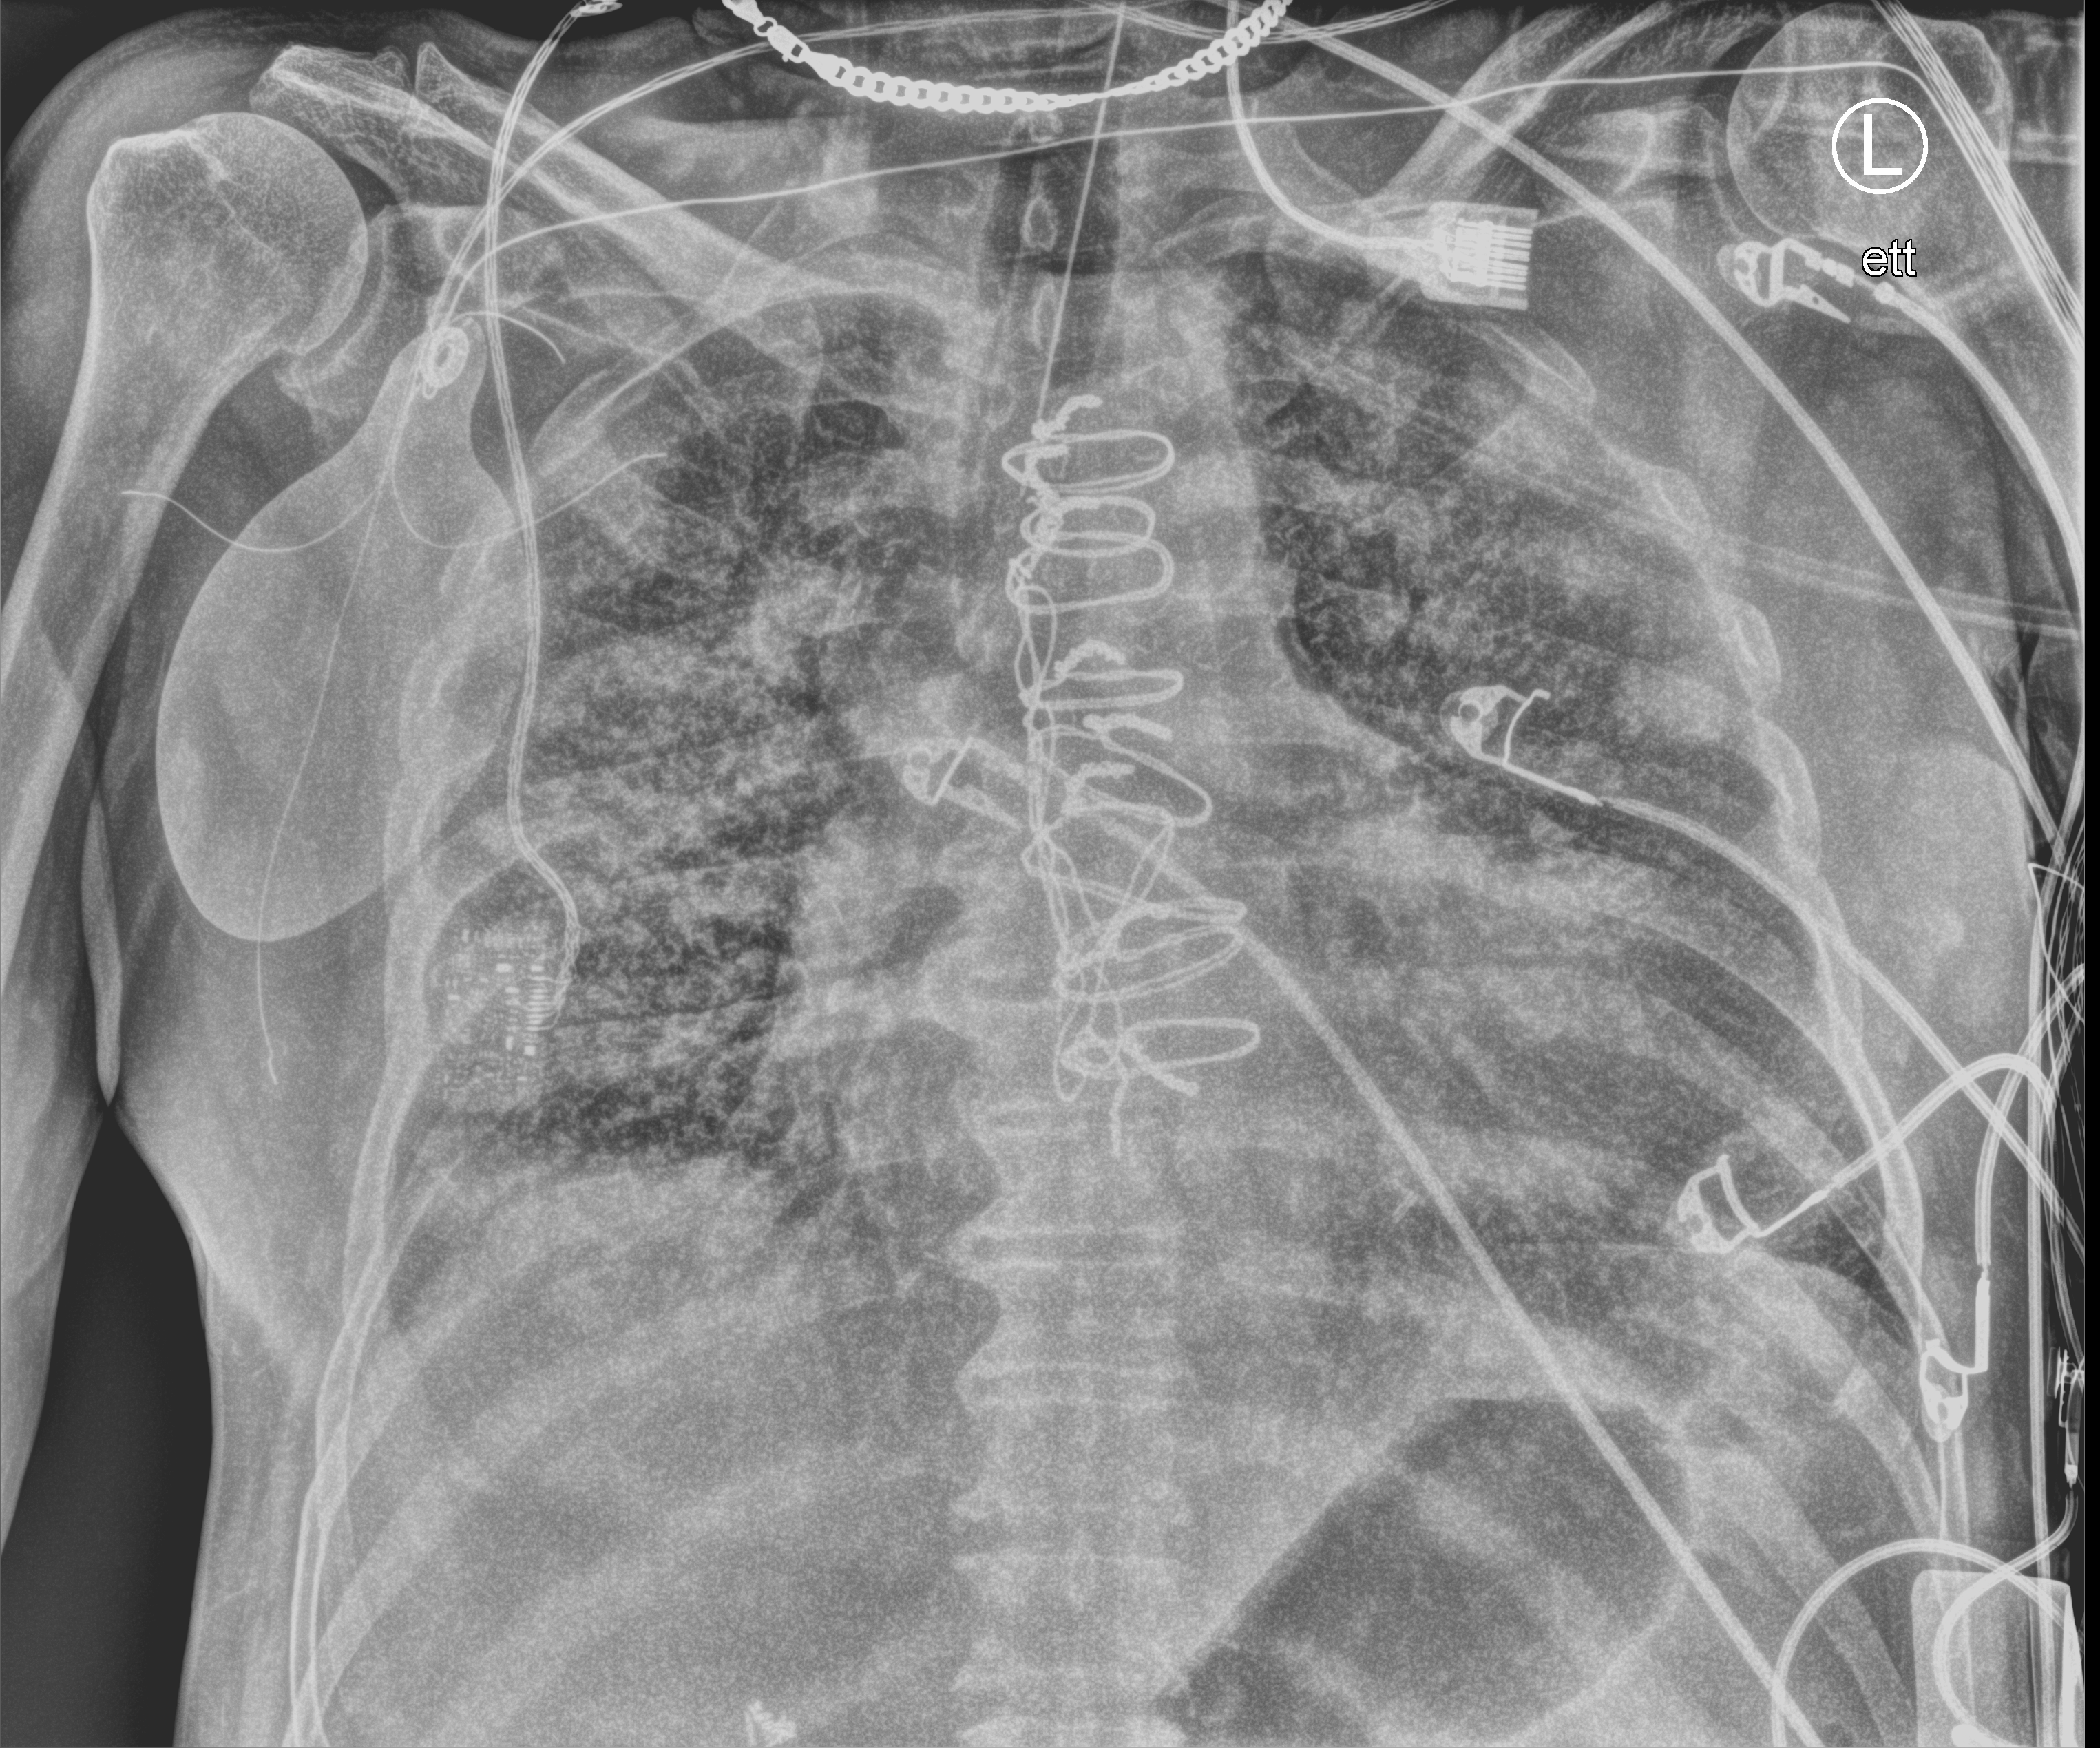
Chest X-ray (portable), anteroposterior (AP) projection. Male patient hospitalised with COVID-19, age 75–90 years.
Hospital-stay facts (about this admission, not read from this image; timing relative to this image not recorded):
- length of hospital stay: 1 day
- admitted to intensive care during this hospital stay: no